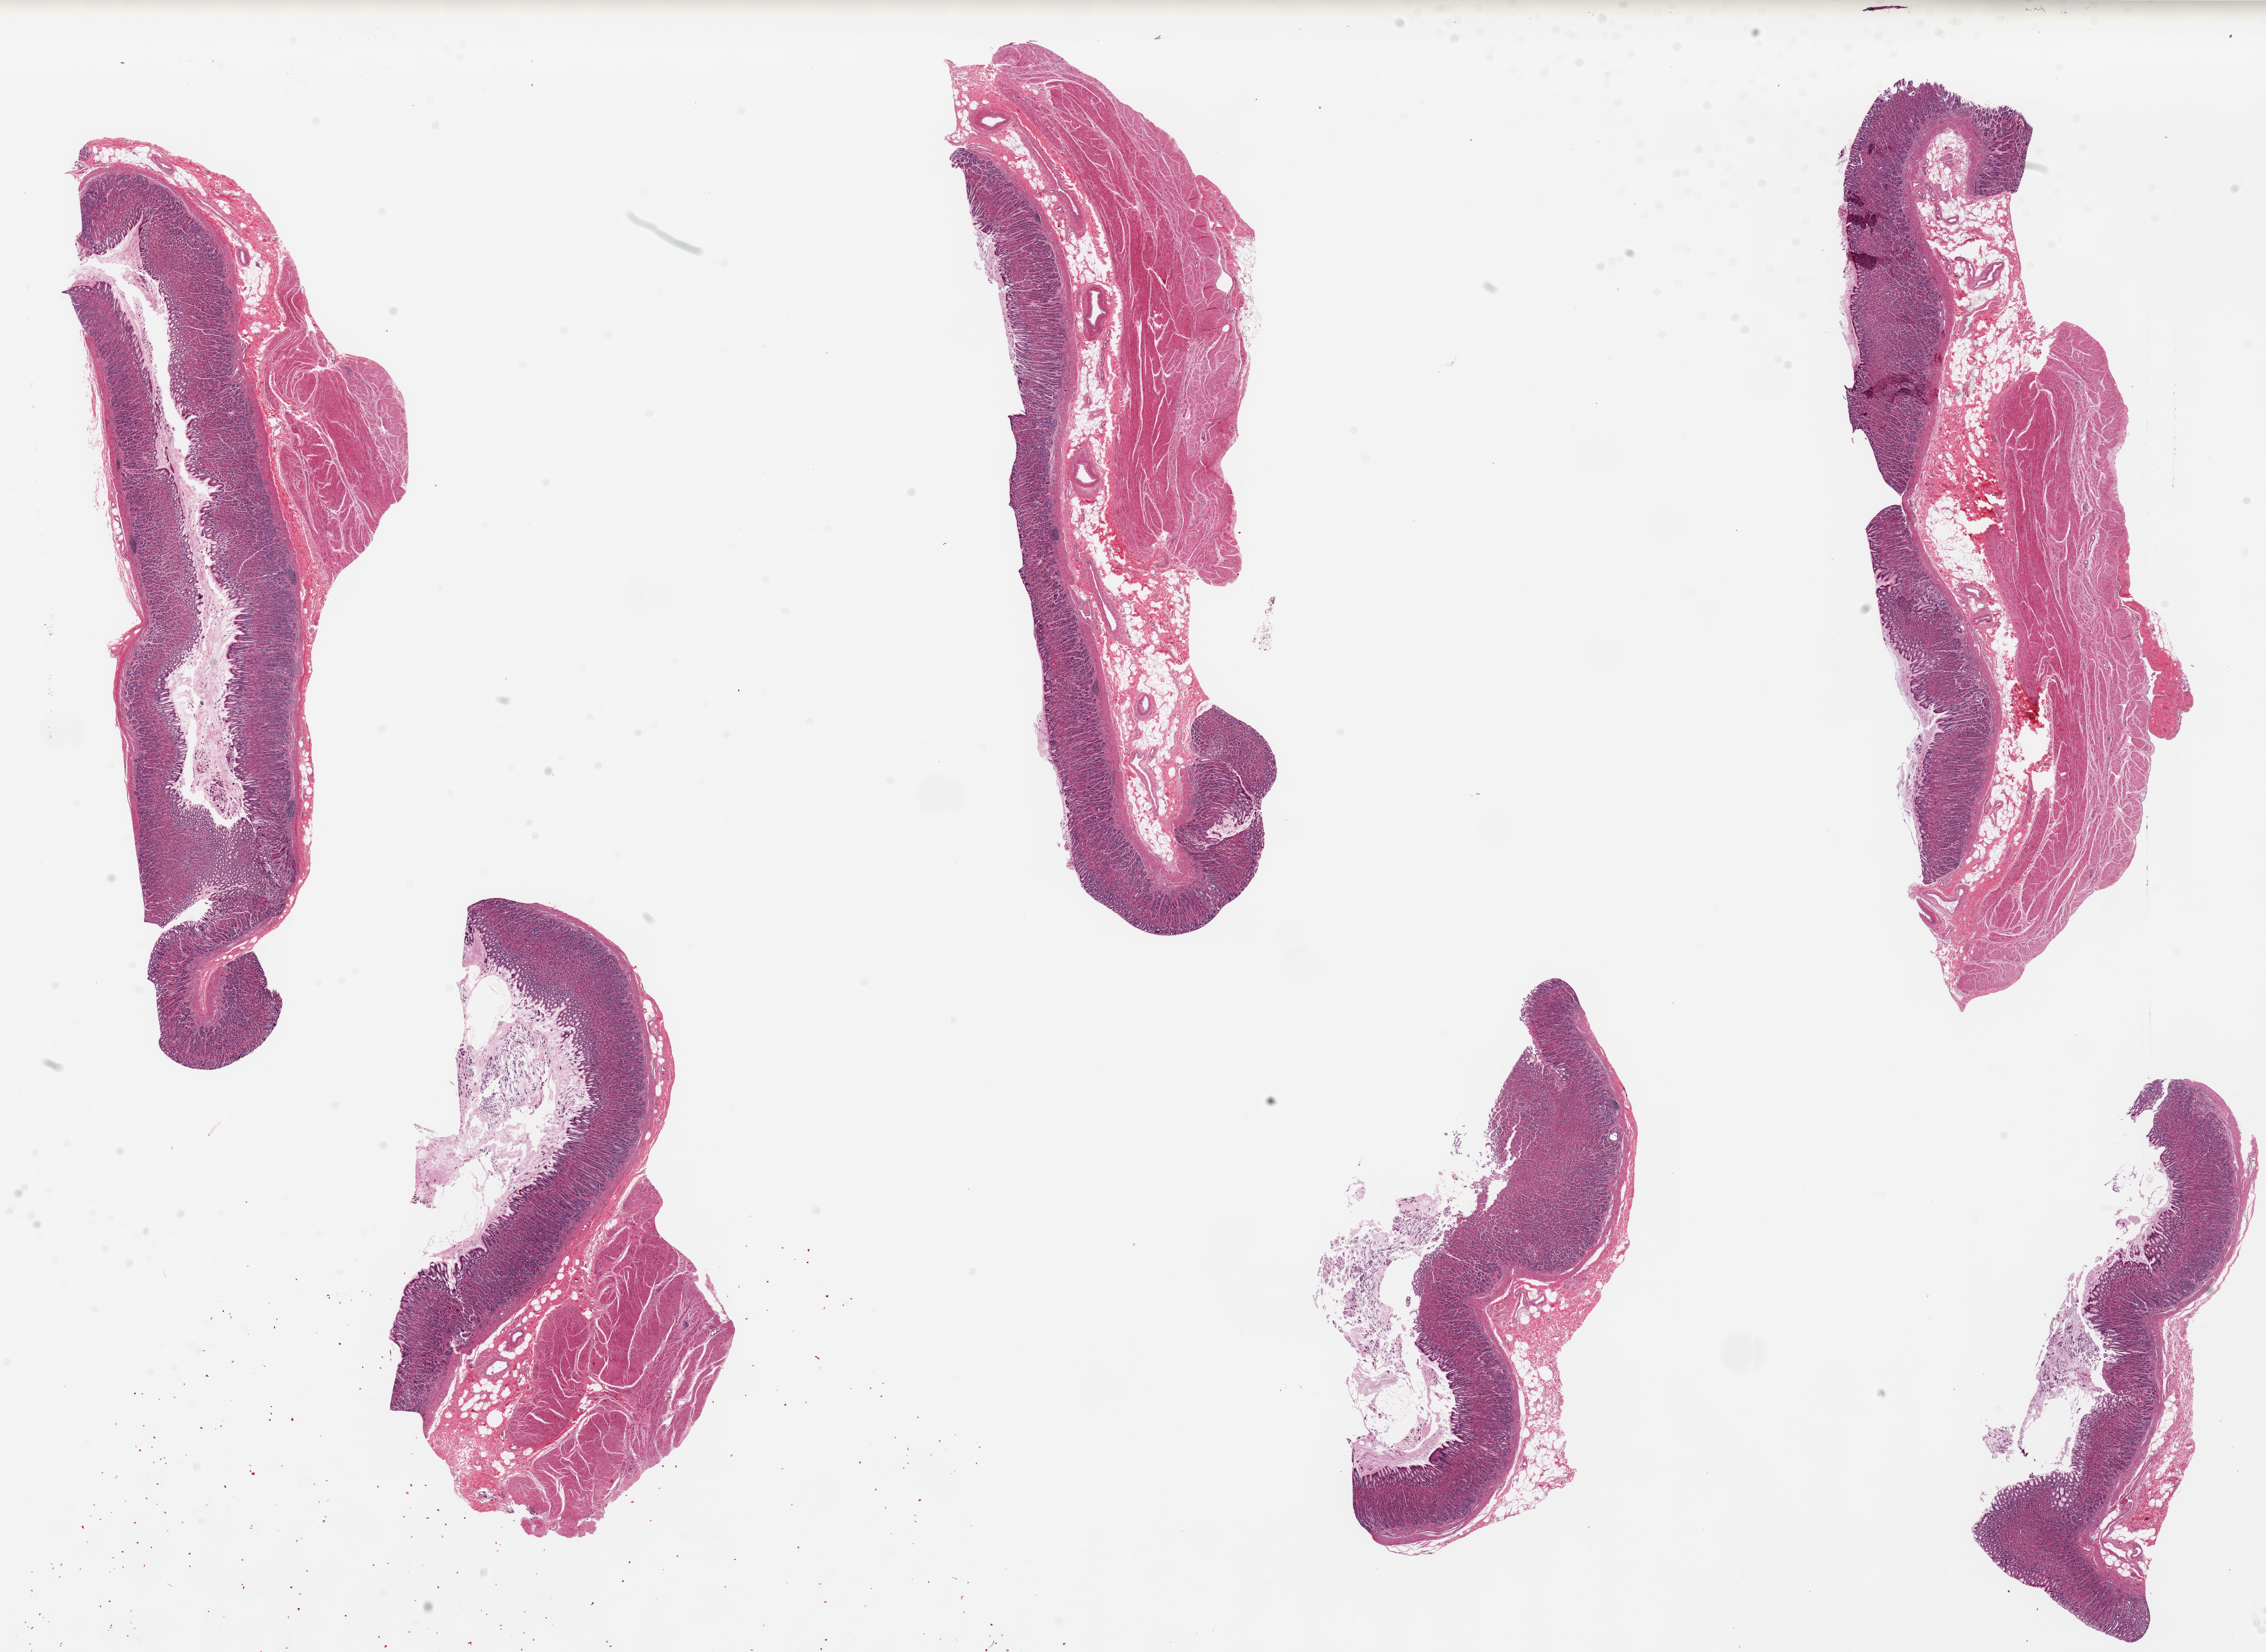
Digitized haematoxylin and eosin-stained section, shown as a low-resolution overview of the whole scanned area (about 30.5 x 22.2 mm); PAXgene-fixed paraffin-embedded (PFPE) section; target tissue: stomach; tissue donor sample.
Pathologist's review note for this sample: 6 pieces, up to 12x4mm; Well preserved mucosa in all. Muscularis in 4/6.